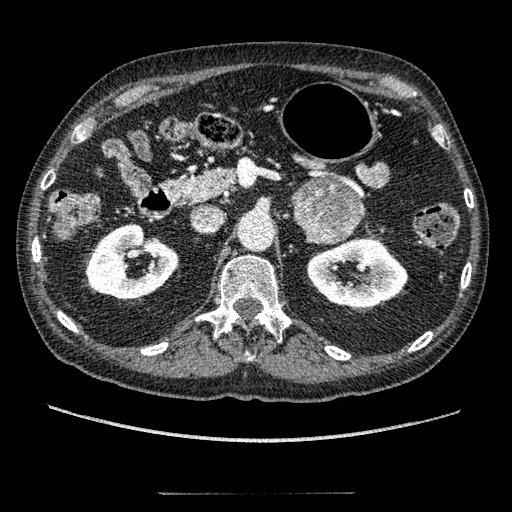
Contrast-enhanced abdominal CT, one axial slice. Position 116 of 274 along the scan axis. Reconstruction kernel STANDARD. Intravenous contrast given. Soft-tissue window (W 400 / L 40 HU). 512 × 512 image matrix. Male patient, age 69 years. Case-level facts recorded for this patient, not image findings: diagnosis: adrenocortical carcinoma; tumour side: left adrenal; tumour size at pathology: 6.1 cm; Ki-67 index: 10 %; stage (as recorded): 3.
Annotated regions visible in this slice (semi-automatically segmented with operator editing):
- mass: bounding box <292,179,365,243> (left, top, right, bottom; pixels)